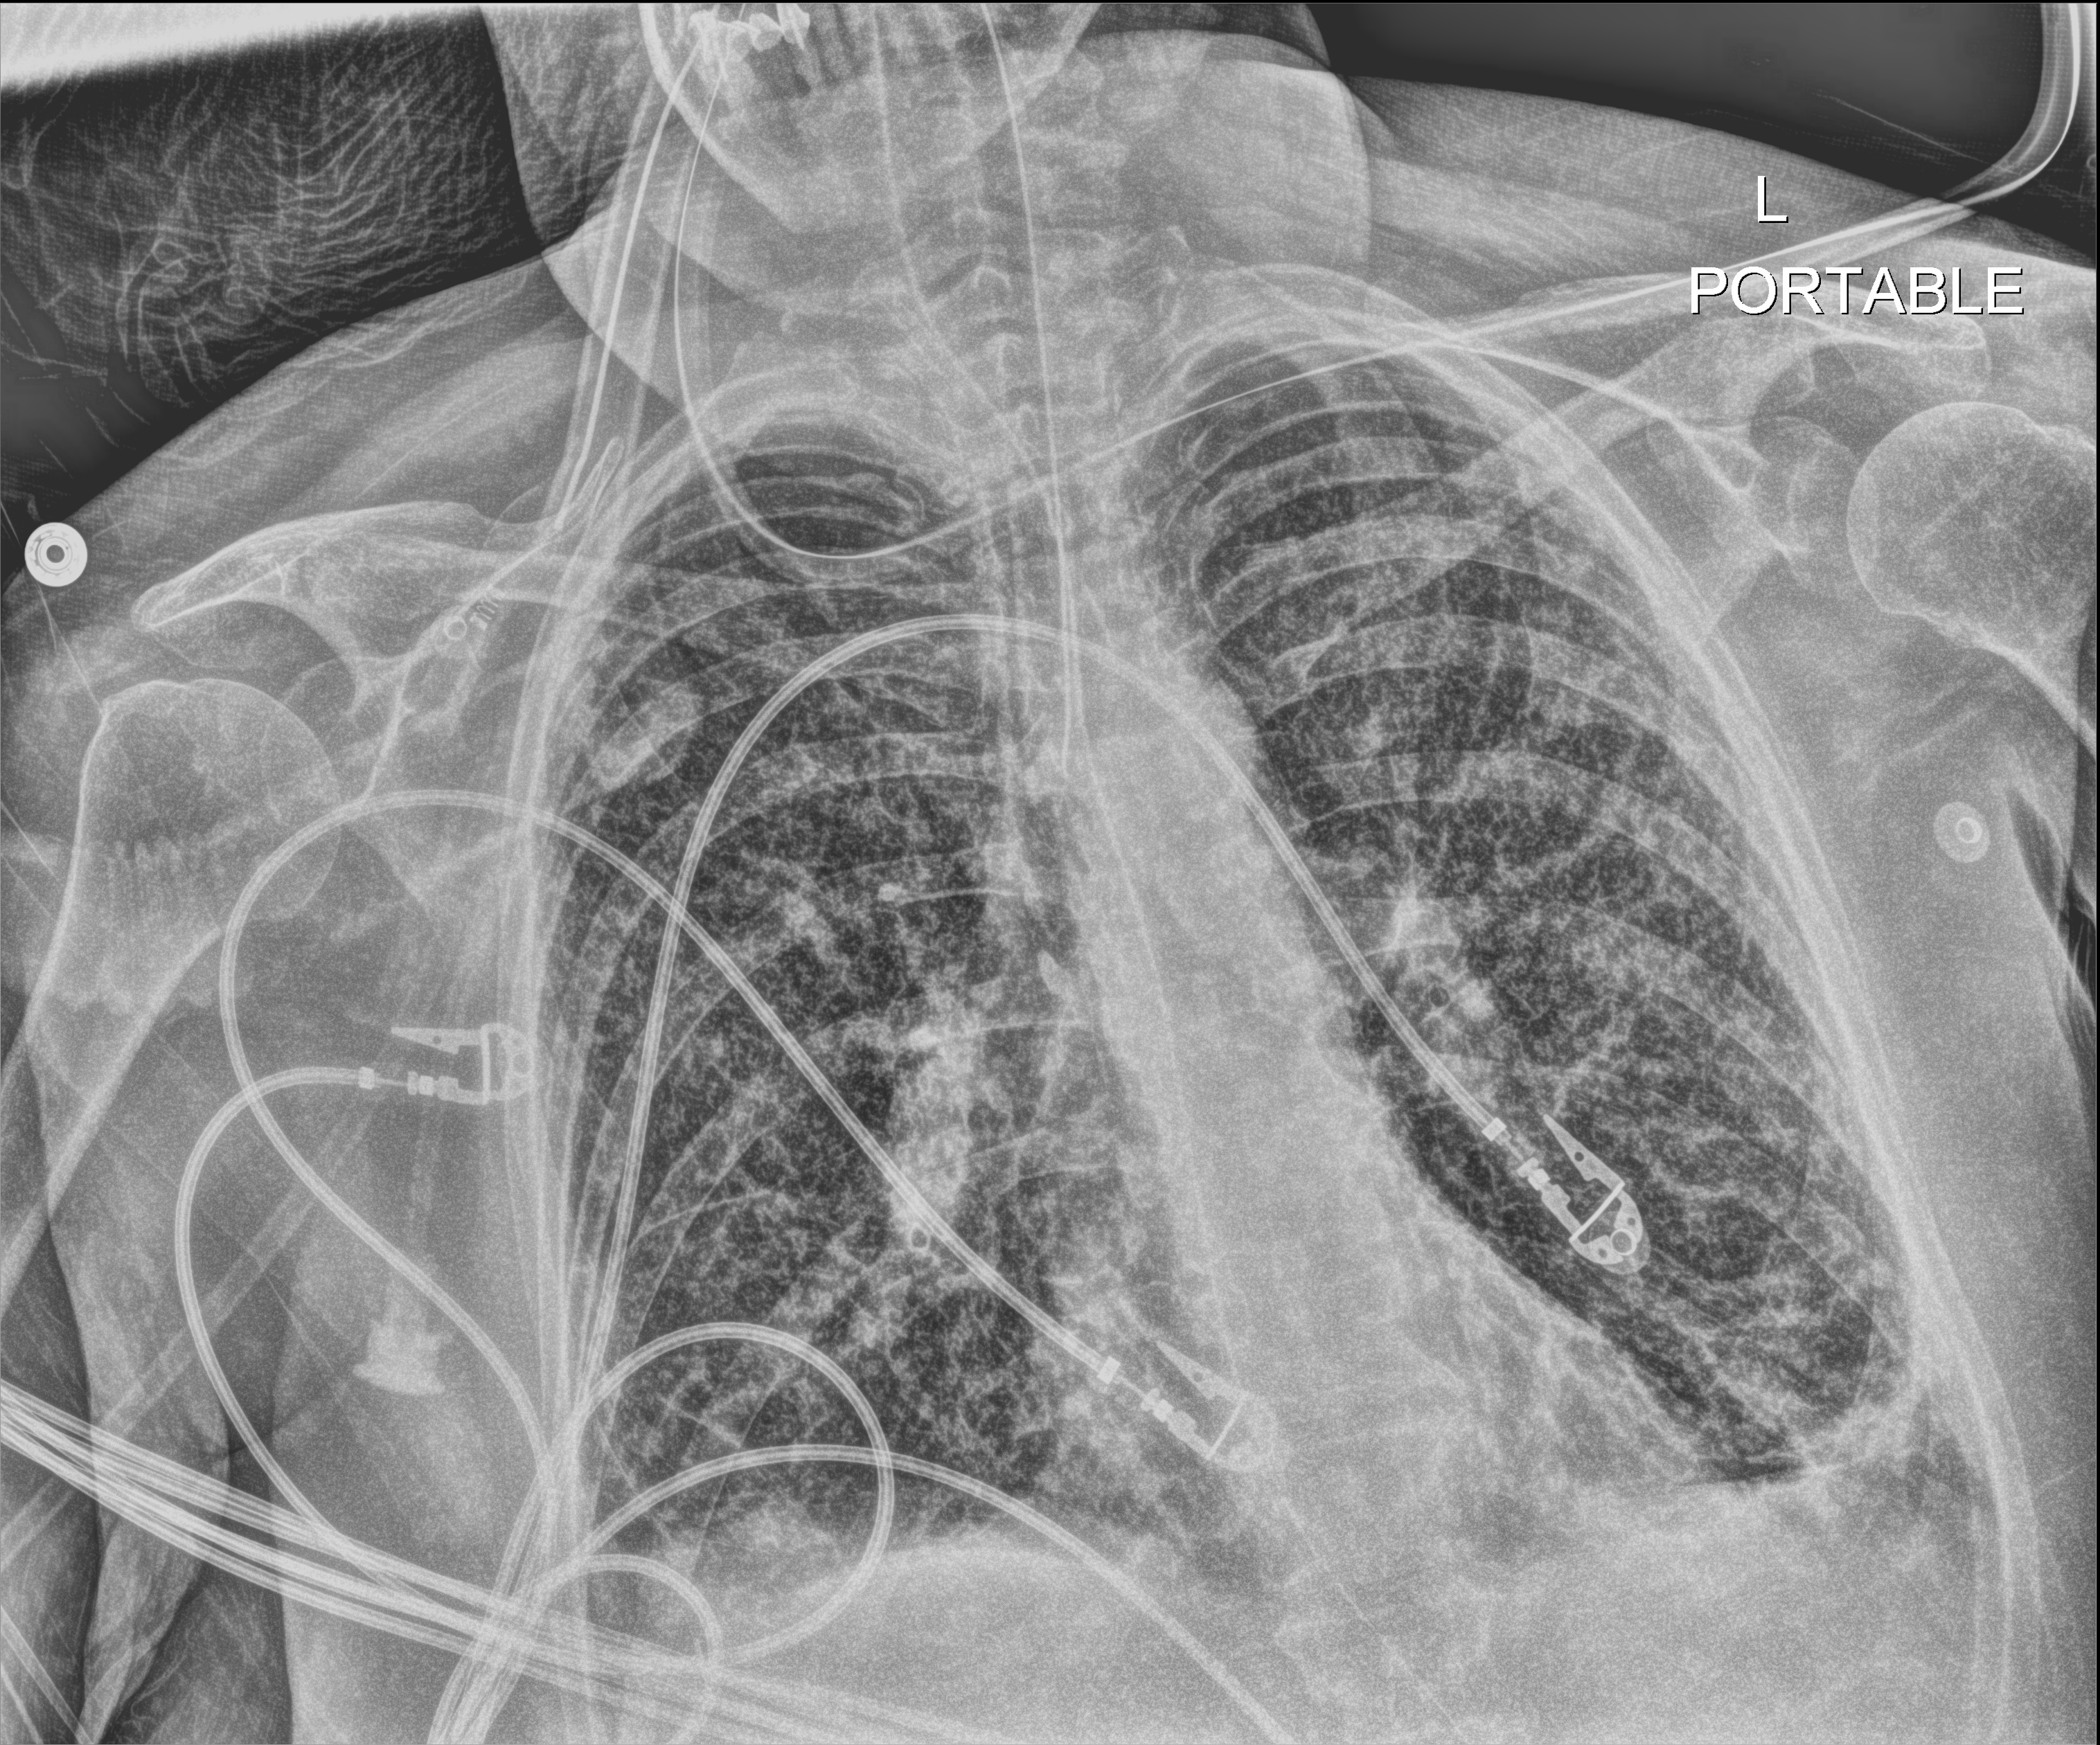
Bedside chest radiograph (digital radiography), anteroposterior (AP) projection. Patient hospitalised with COVID-19; female, aged 60–74 years.
Hospital-stay facts (about this admission, not read from this image; timing relative to this image not recorded): admitted to intensive care during this hospital stay: yes; COPD (admission record): yes; mechanically ventilated during this hospital stay: yes.